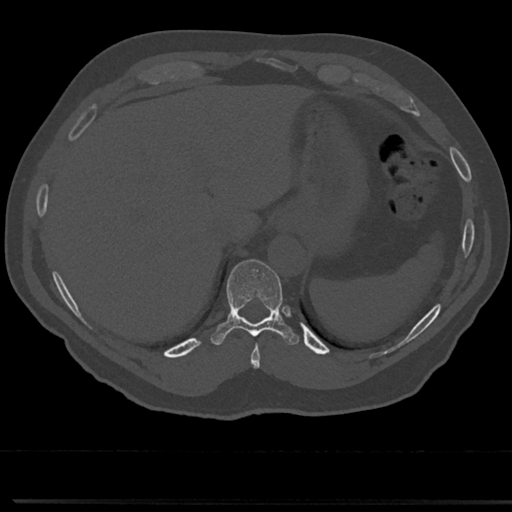
CT including the spine, one axial slice; position 259 of 817 along the scan axis; 120 kVp; bone window (W 1800 / L 400 HU); 0.5 mm slice thickness; 512 × 512 image matrix, field of view 355 × 355 mm. Male patient, age 61 years. From the clinical record (not read from this slice): primary cancer: prostate.
Outlined on this slice (semi-automatically segmented with operator editing):
- T10 vertebra: box from (x=211, y=260) to (x=299, y=345) px
- T9 vertebra: (x=251, y=332)–(x=263, y=366)